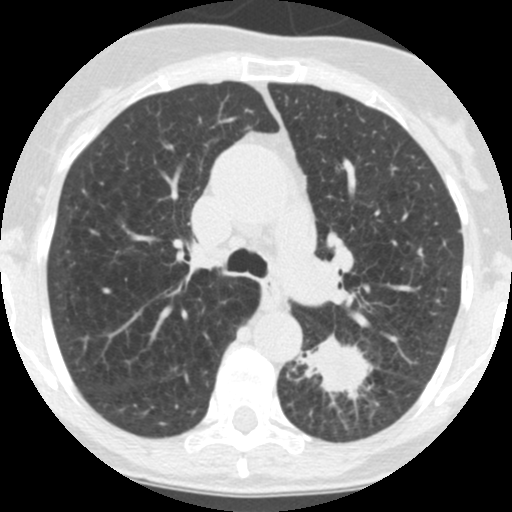
Axial slice from a low-dose chest CT screening exam; third screening round (two years after baseline); lung window (W 1500 / L -600 HU); 2.5 mm slice thickness; standard (soft-tissue) reconstruction kernel (STANDARD); 120 kVp; slice 56 of 171 in the series; 512 × 512 image matrix. Female, age 71 years at enrolment. Current smoker at enrolment.
- Expert reader's lesion annotation, bounding box <300,329,381,410> (left, top, right, bottom; pixels).
- The screening reader recorded 2 non-calcified nodules or masses ≥4 mm on this exam (left lower lobe, left lower lobe); which of them this box marks is not recorded.
- Official screen result: positive, other.
- Participant outcome: lung cancer diagnosed 26 days after this screen — squamous cell carcinoma, NOS, left lower lobe, poorly differentiated (G3), stage IB (AJCC 6th edition), 40 mm at pathology.